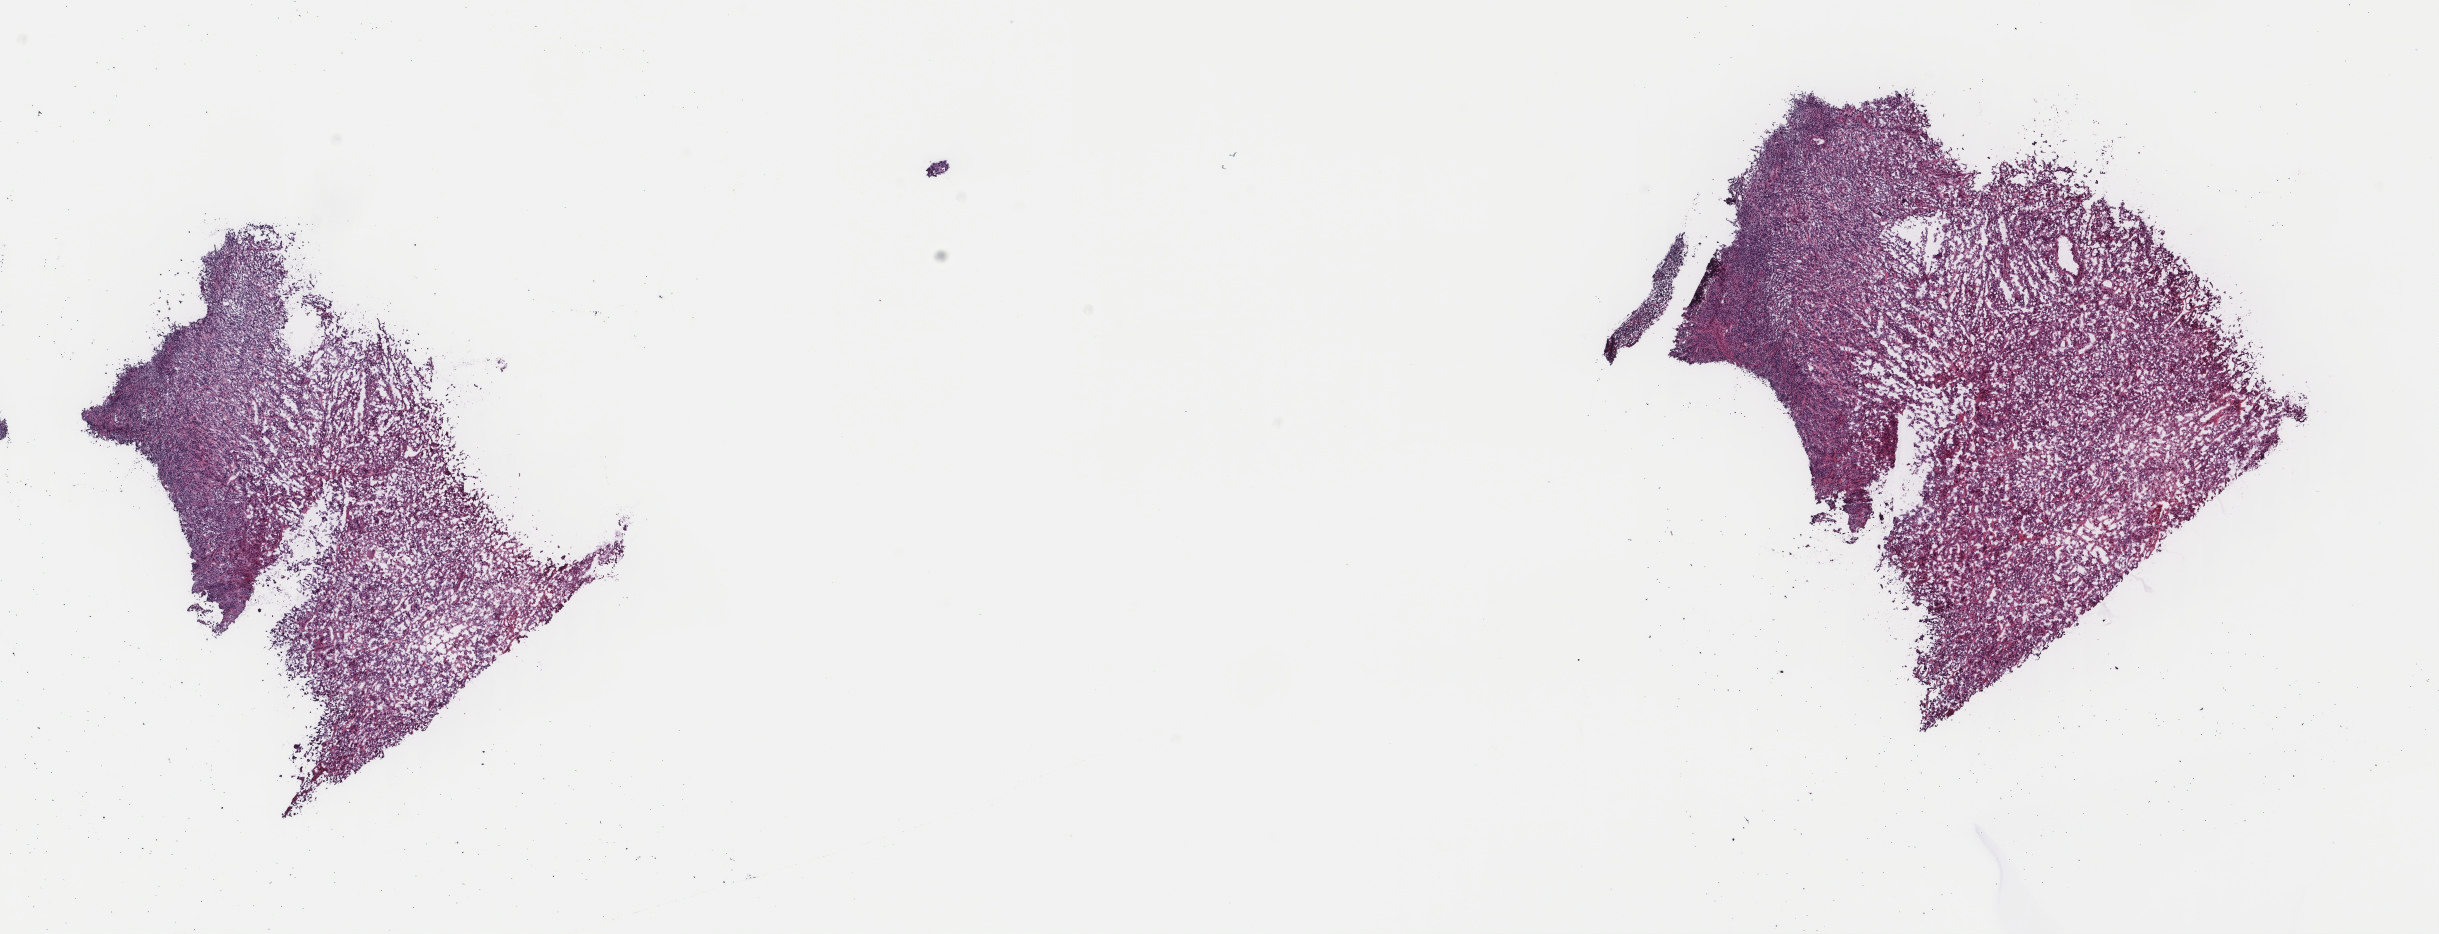
H&E whole-slide image, low-resolution overview of the scanned area, about 19.4 x 7.4 mm, frozen section, metastatic tumour sample, sampled site not recorded. Patient: male, age at initial diagnosis 70 years. Slide review estimates, as recorded: tumour cells 100%, tumour nuclei 90%, normal cells 0%, stromal cells 0%, necrosis 0%. Infiltration values recorded for this section: lymphocyte infiltration 5%, monocyte infiltration 0%, neutrophil infiltration 0%.
This section: metastatic tumour tissue. Patient diagnosis: Malignant melanoma, NOS.